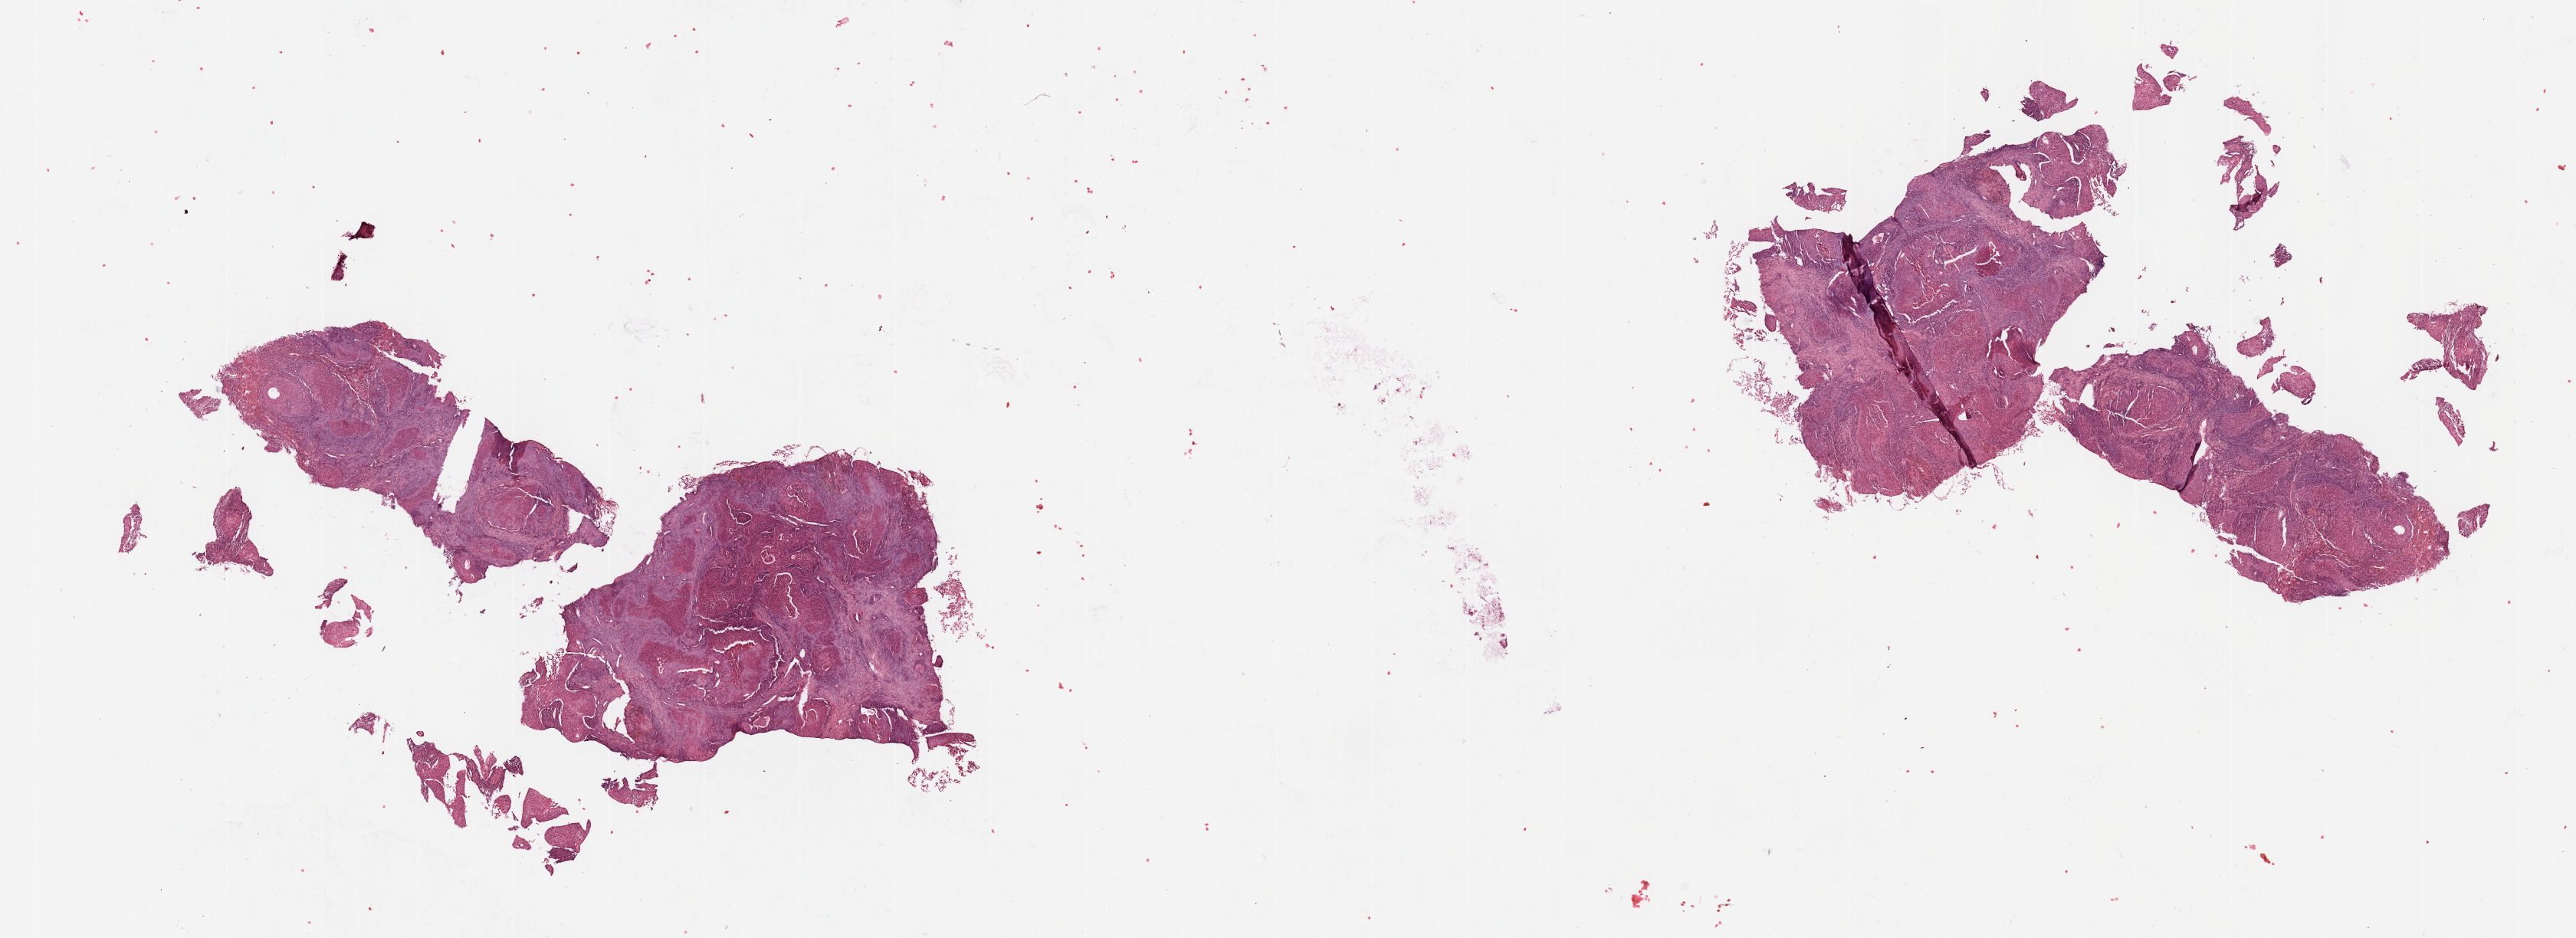
Whole-slide histology image, H&E — a low-resolution overview of the entire scanned area, about 26.6 x 9.7 mm (slide scanned at 20x). Tumour tissue sample, sampled site: lung. 69-year-old male patient. Histologic grade: G3 (poorly differentiated). Pathologist review of this section (percent, as recorded): tumour nuclei 75%, necrosis 5%.
* AJCC pathologic stage: IA
* histologic diagnosis: Squamous cell carcinoma, NOS
* primary tumour site (as recorded): right lower lobe